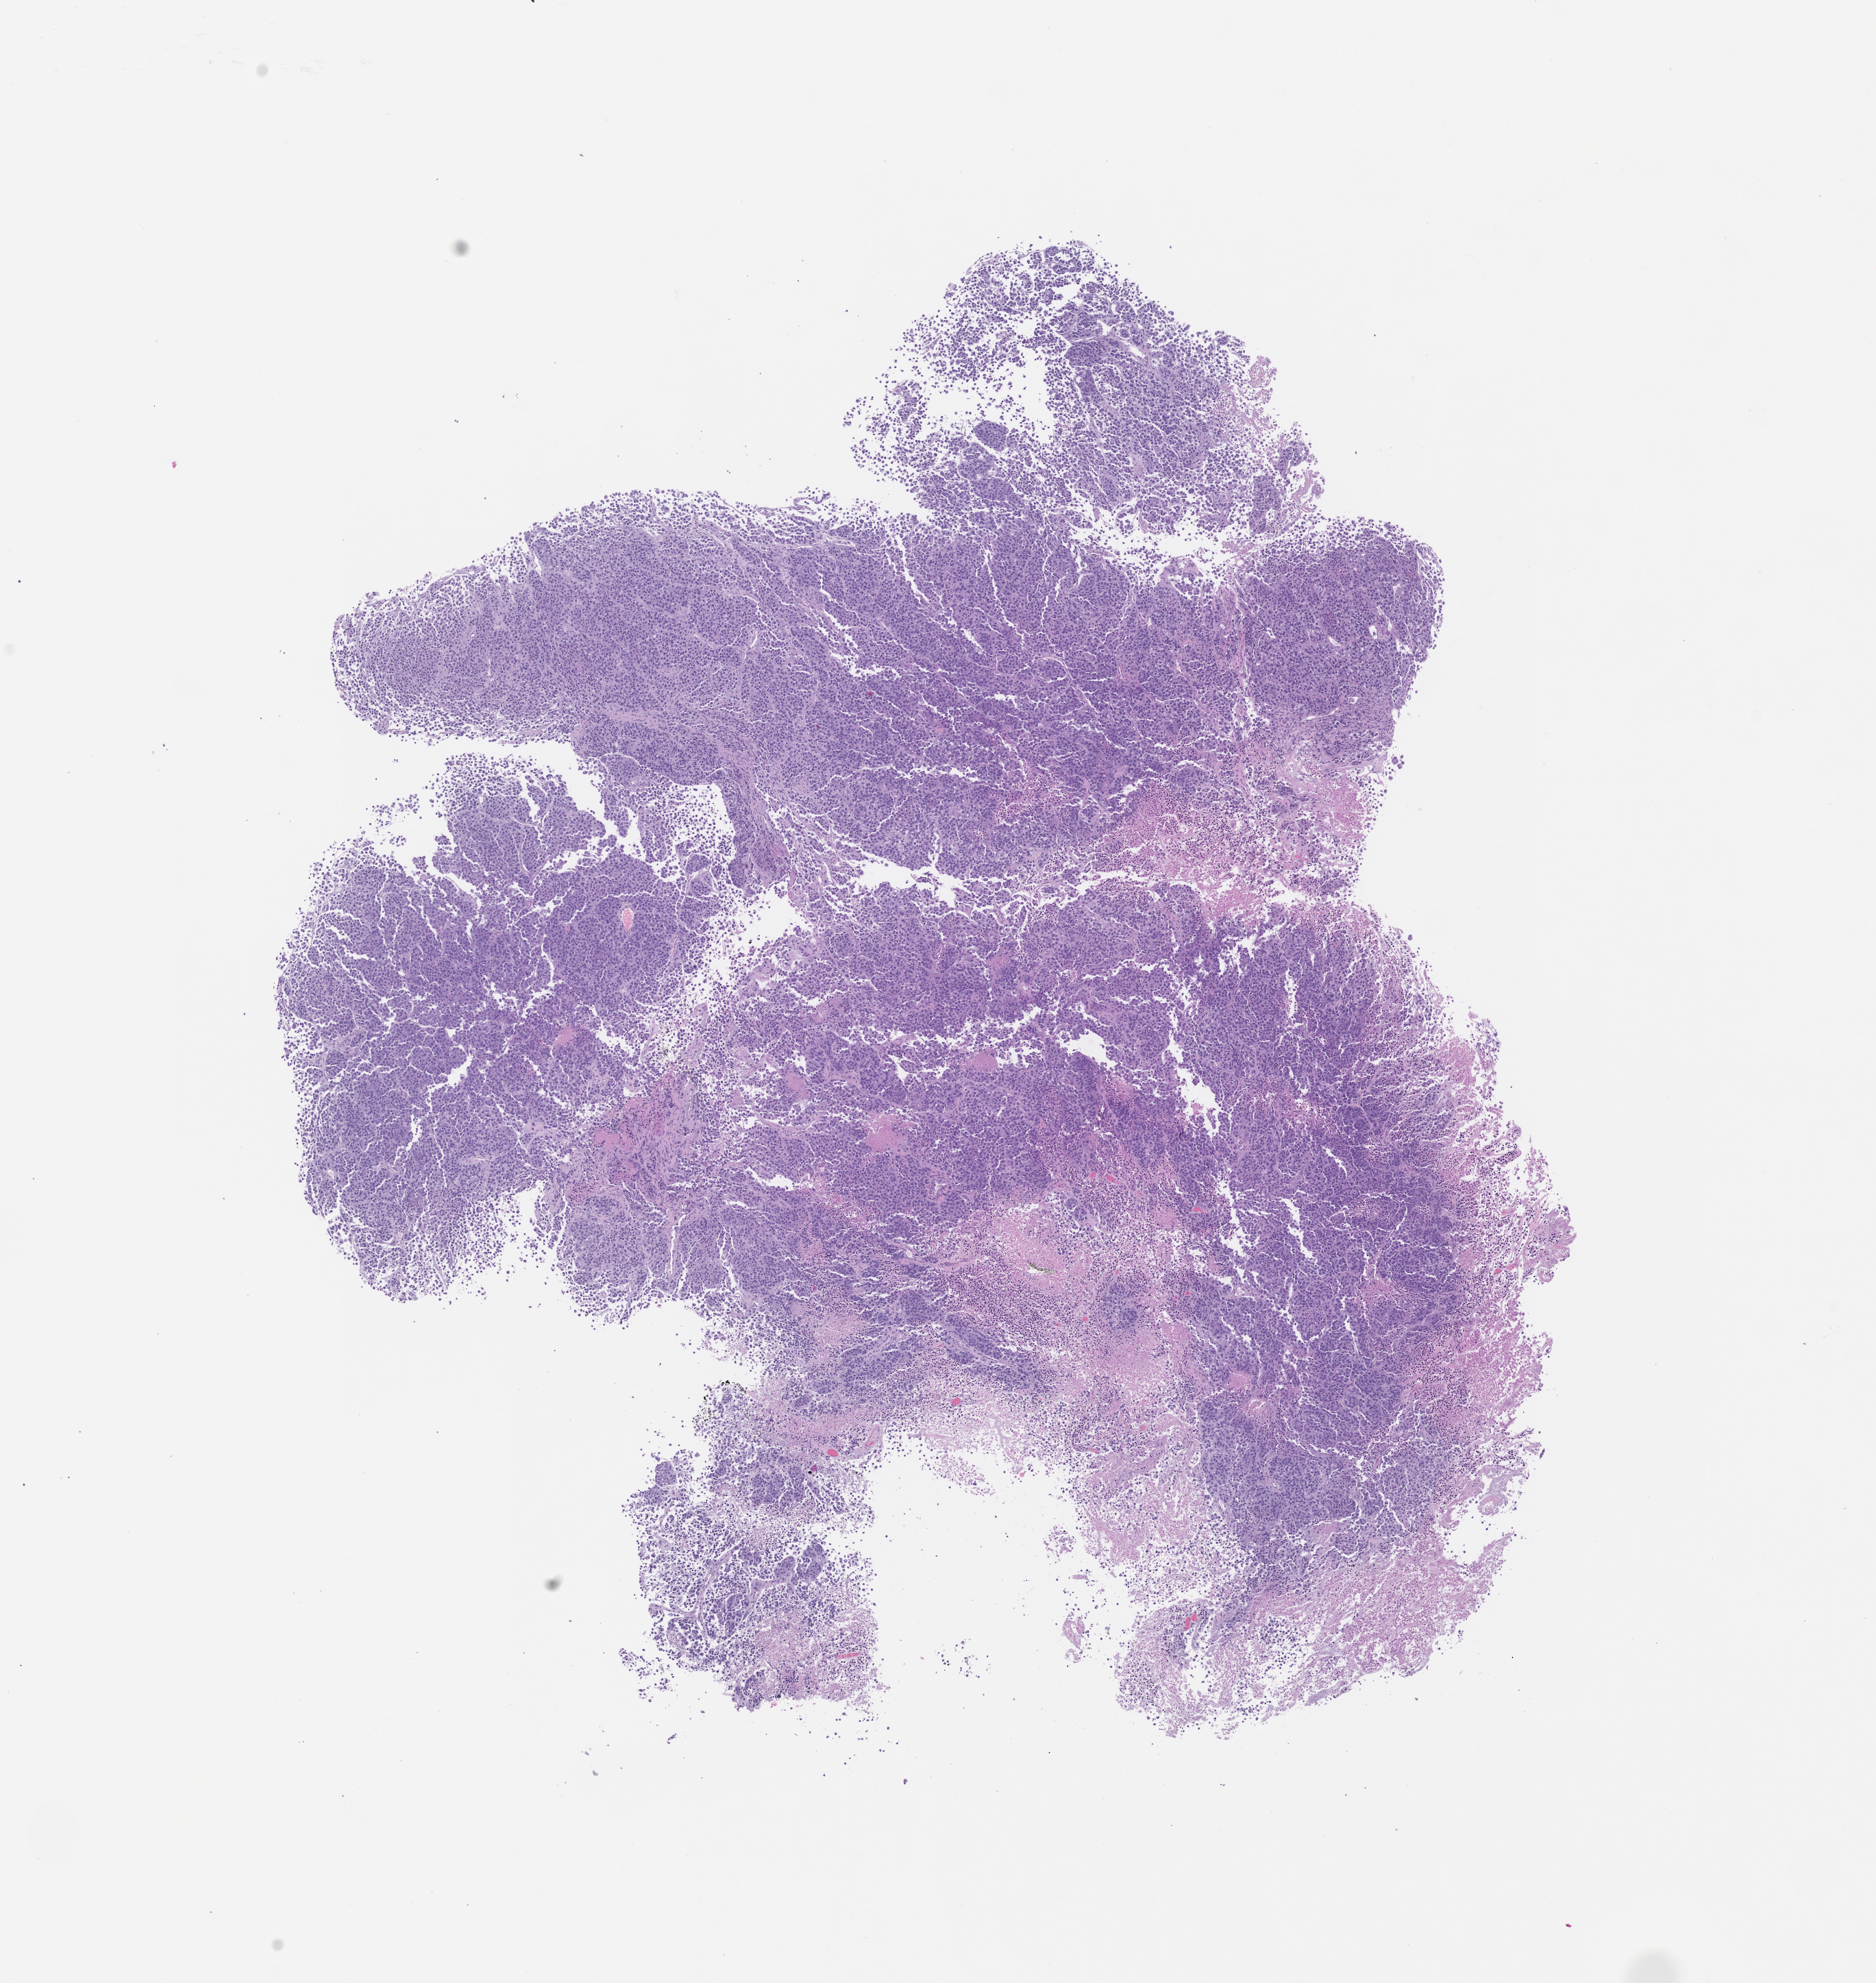
H&E whole-slide image of a patient-derived xenograft (PDX) tumor grown in a mouse, passage 3, shown as a low-resolution overview of the whole scanned area (about 11.0 x 11.6 mm). Formalin-fixed paraffin-embedded section. Originating tumor site category: skin.
• originating patient diagnosis: Melanoma